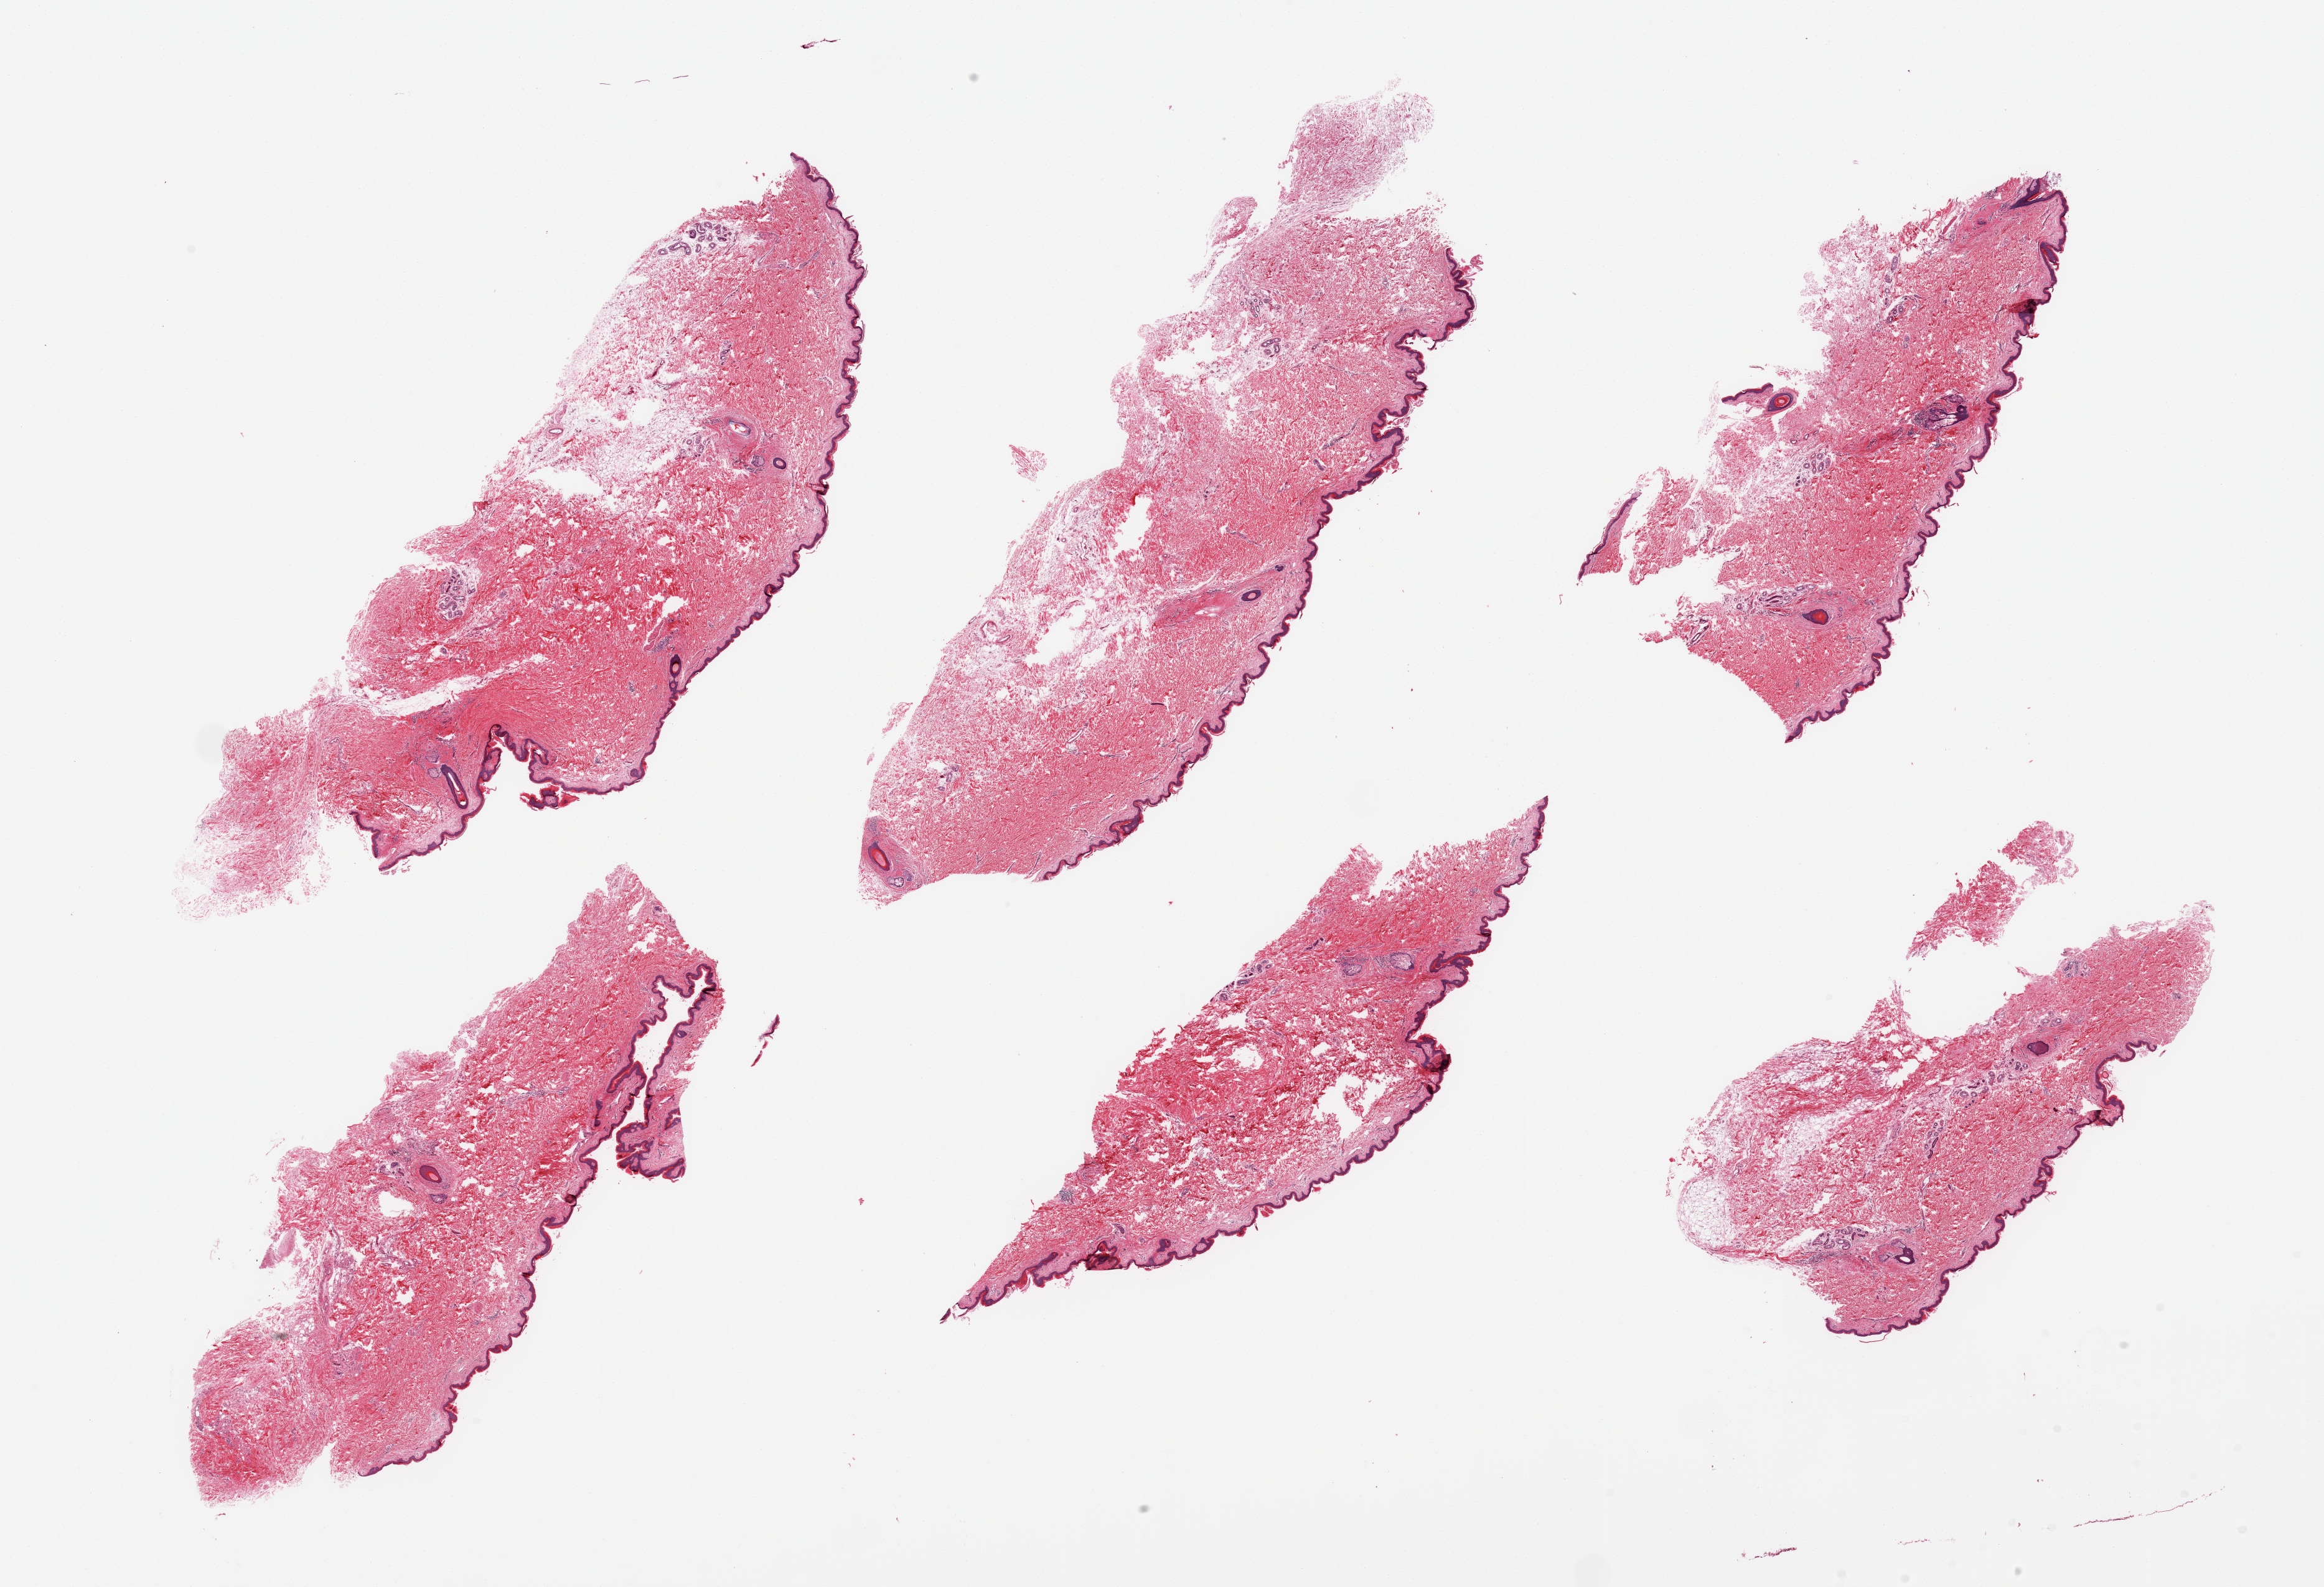
H&E whole-slide image, shown as a low-resolution overview of the whole scanned area (about 29.5 x 20.2 mm, from a 20x scan), PAXgene-fixed paraffin-embedded (PFPE) section, sampled site (target tissue): skin of suprapubic region, tissue donor sample. Male donor.
Reviewer comment on this tissue sample: 6 pieces, no significant dermal fat; squamous epithelium is ~25-36 microns.